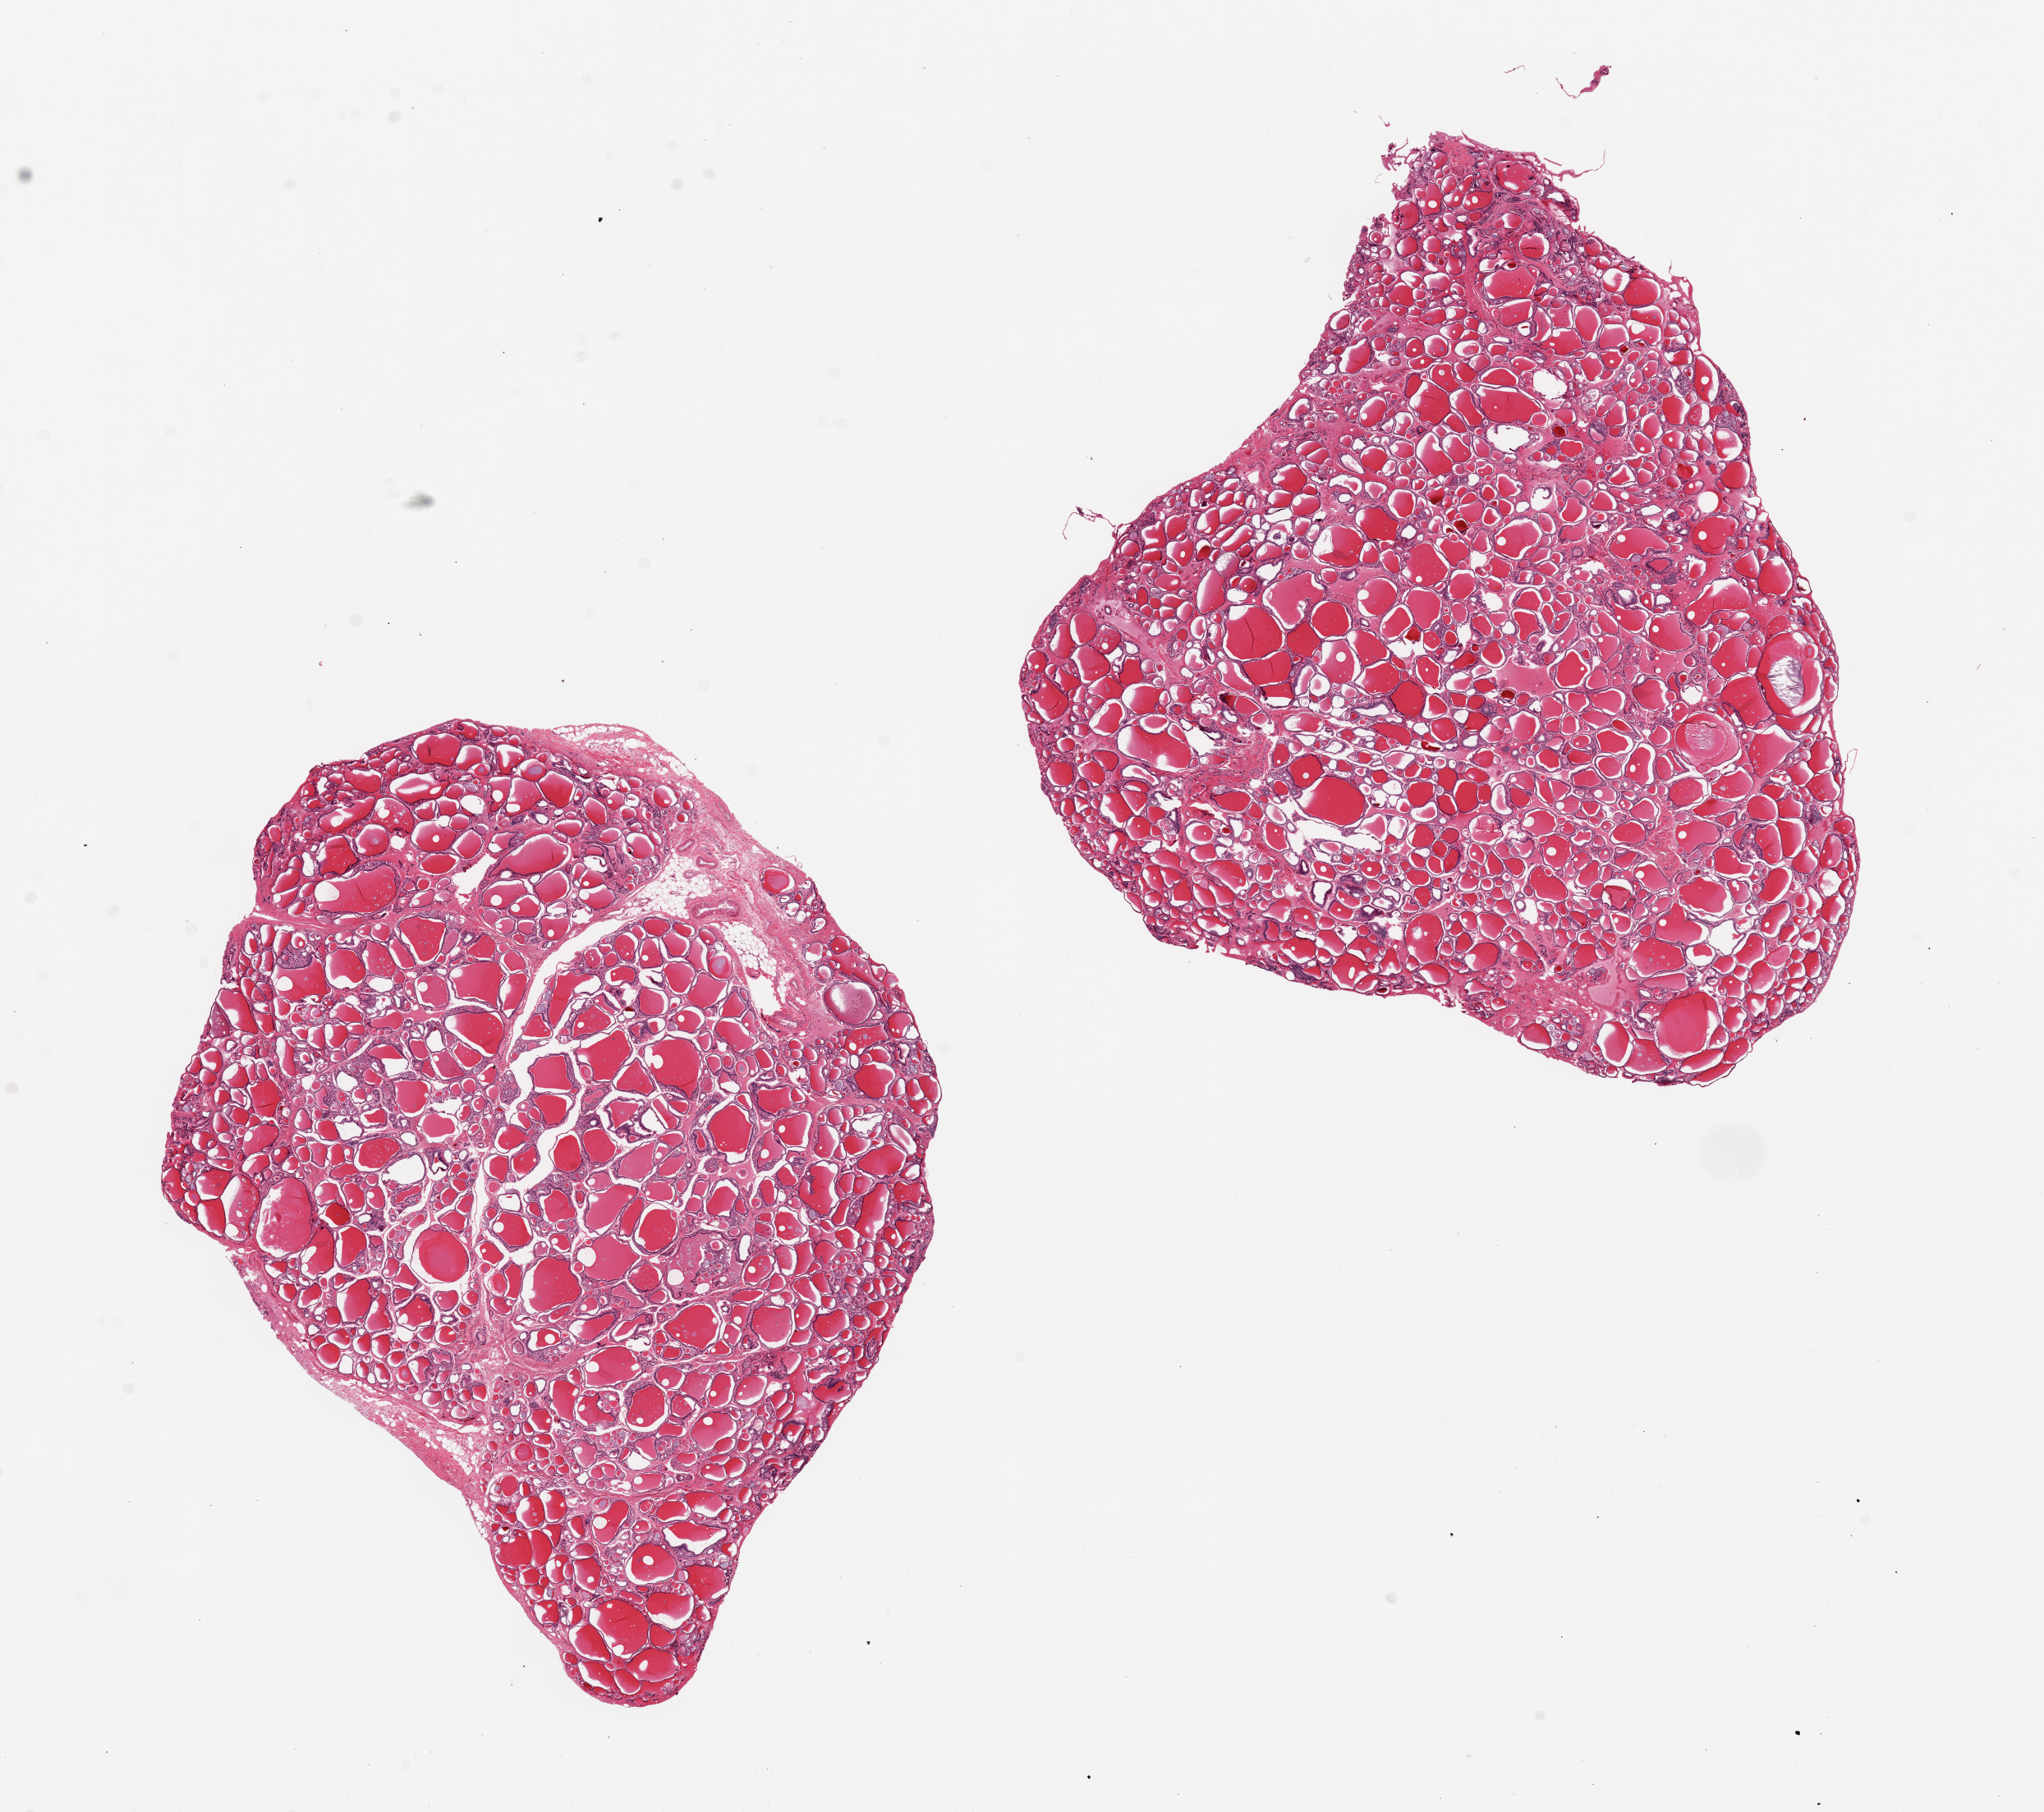
Hematoxylin and eosin (H&E) whole-slide image — low-resolution overview of the scanned area, about 19.7 x 17.5 mm. PAXgene-fixed, paraffin-embedded tissue. Target tissue: thyroid. Donor tissue sample. Female donor.
Pathologist's review note for this sample: 2 pieces, 10x7 & 10x8mm; well trimmed, no adipose.